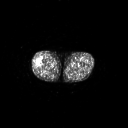
FDG PET of an extremity soft-tissue mass (from a PET/CT study), one axial slice; slice 227 of 267 in the series (ordered by position); 128 × 128 image matrix, field of view 700 × 700 mm. Male patient, age 43 years. From the clinical record (not read from this slice): histological type: poorly differentiated synovial sarcoma; grade: high; site of the primary tumour: right buttock.
Outlined on this slice (expert contour drawn on MRI and transferred to this co-registered scan by the dataset authors):
- gross tumour volume including surrounding oedema: bounding box <34,59,43,69> (left, top, right, bottom; pixels)